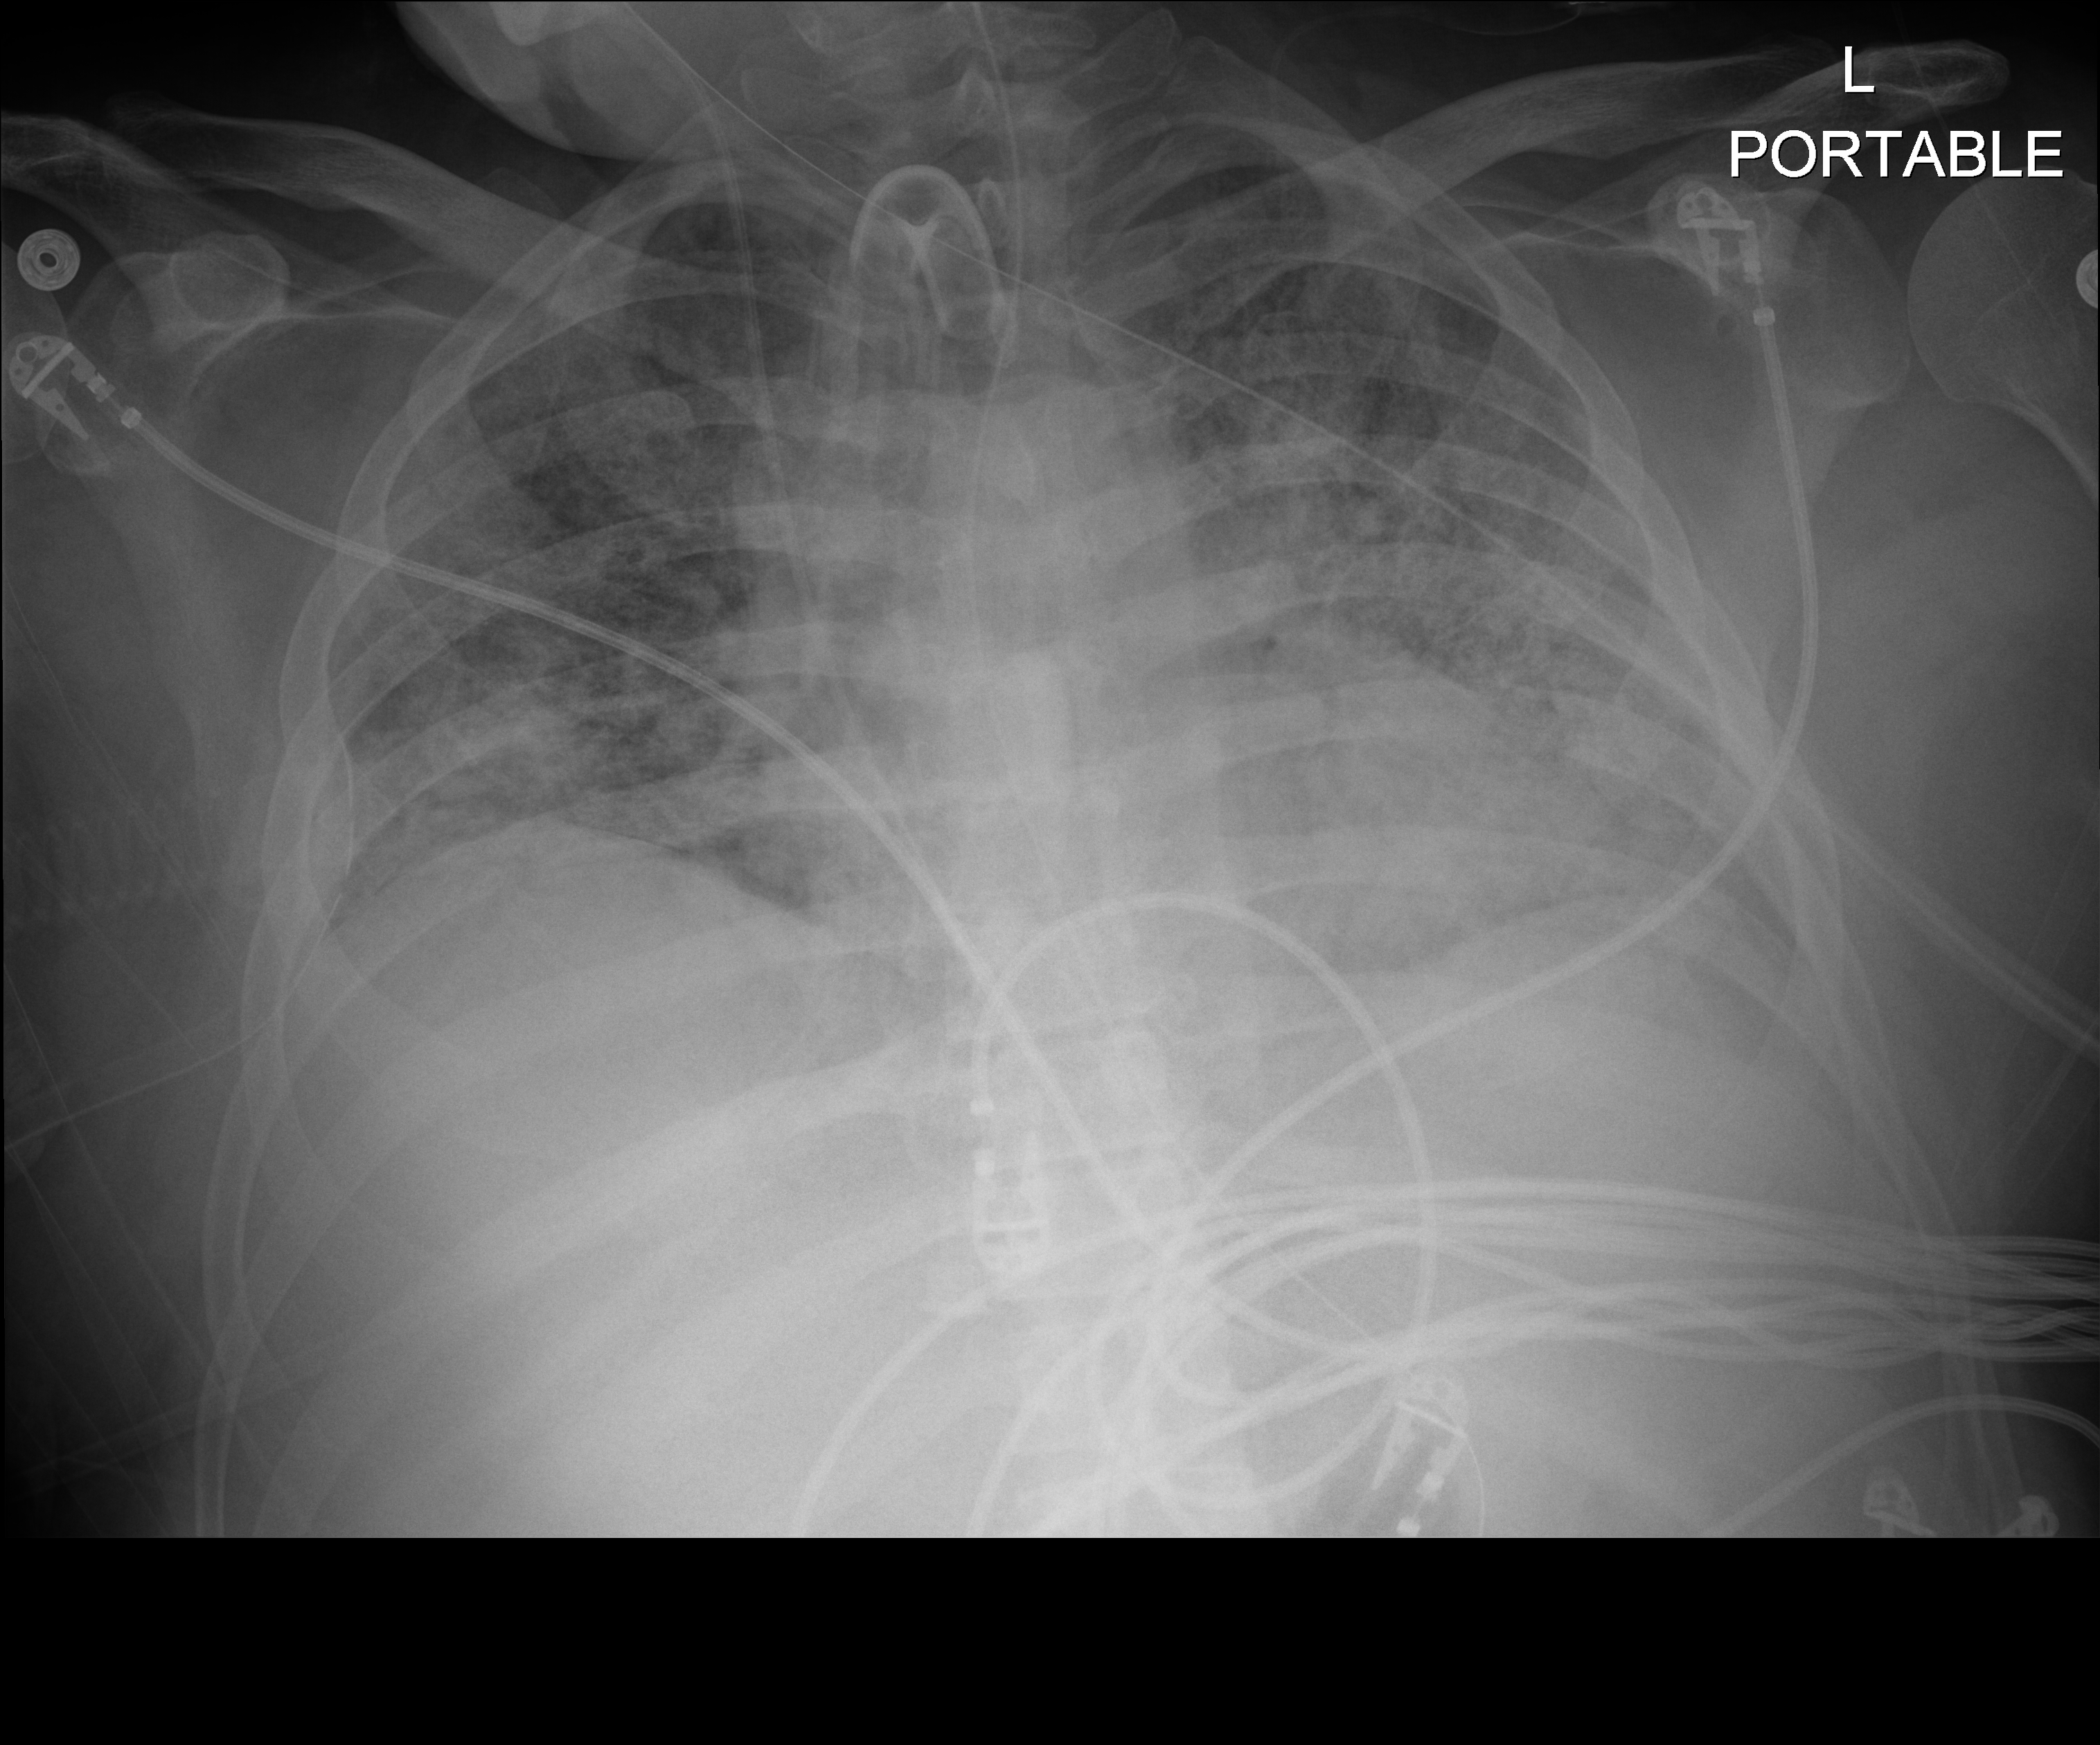
Chest radiograph; anteroposterior (AP) projection. Patient hospitalised with COVID-19; male, aged 18–59 years.
Hospital-stay facts (about this admission, not read from this image; timing relative to this image not recorded): other chronic lung disease (admission record): no; smoking status (admission record): never; mechanically ventilated during this hospital stay: yes.